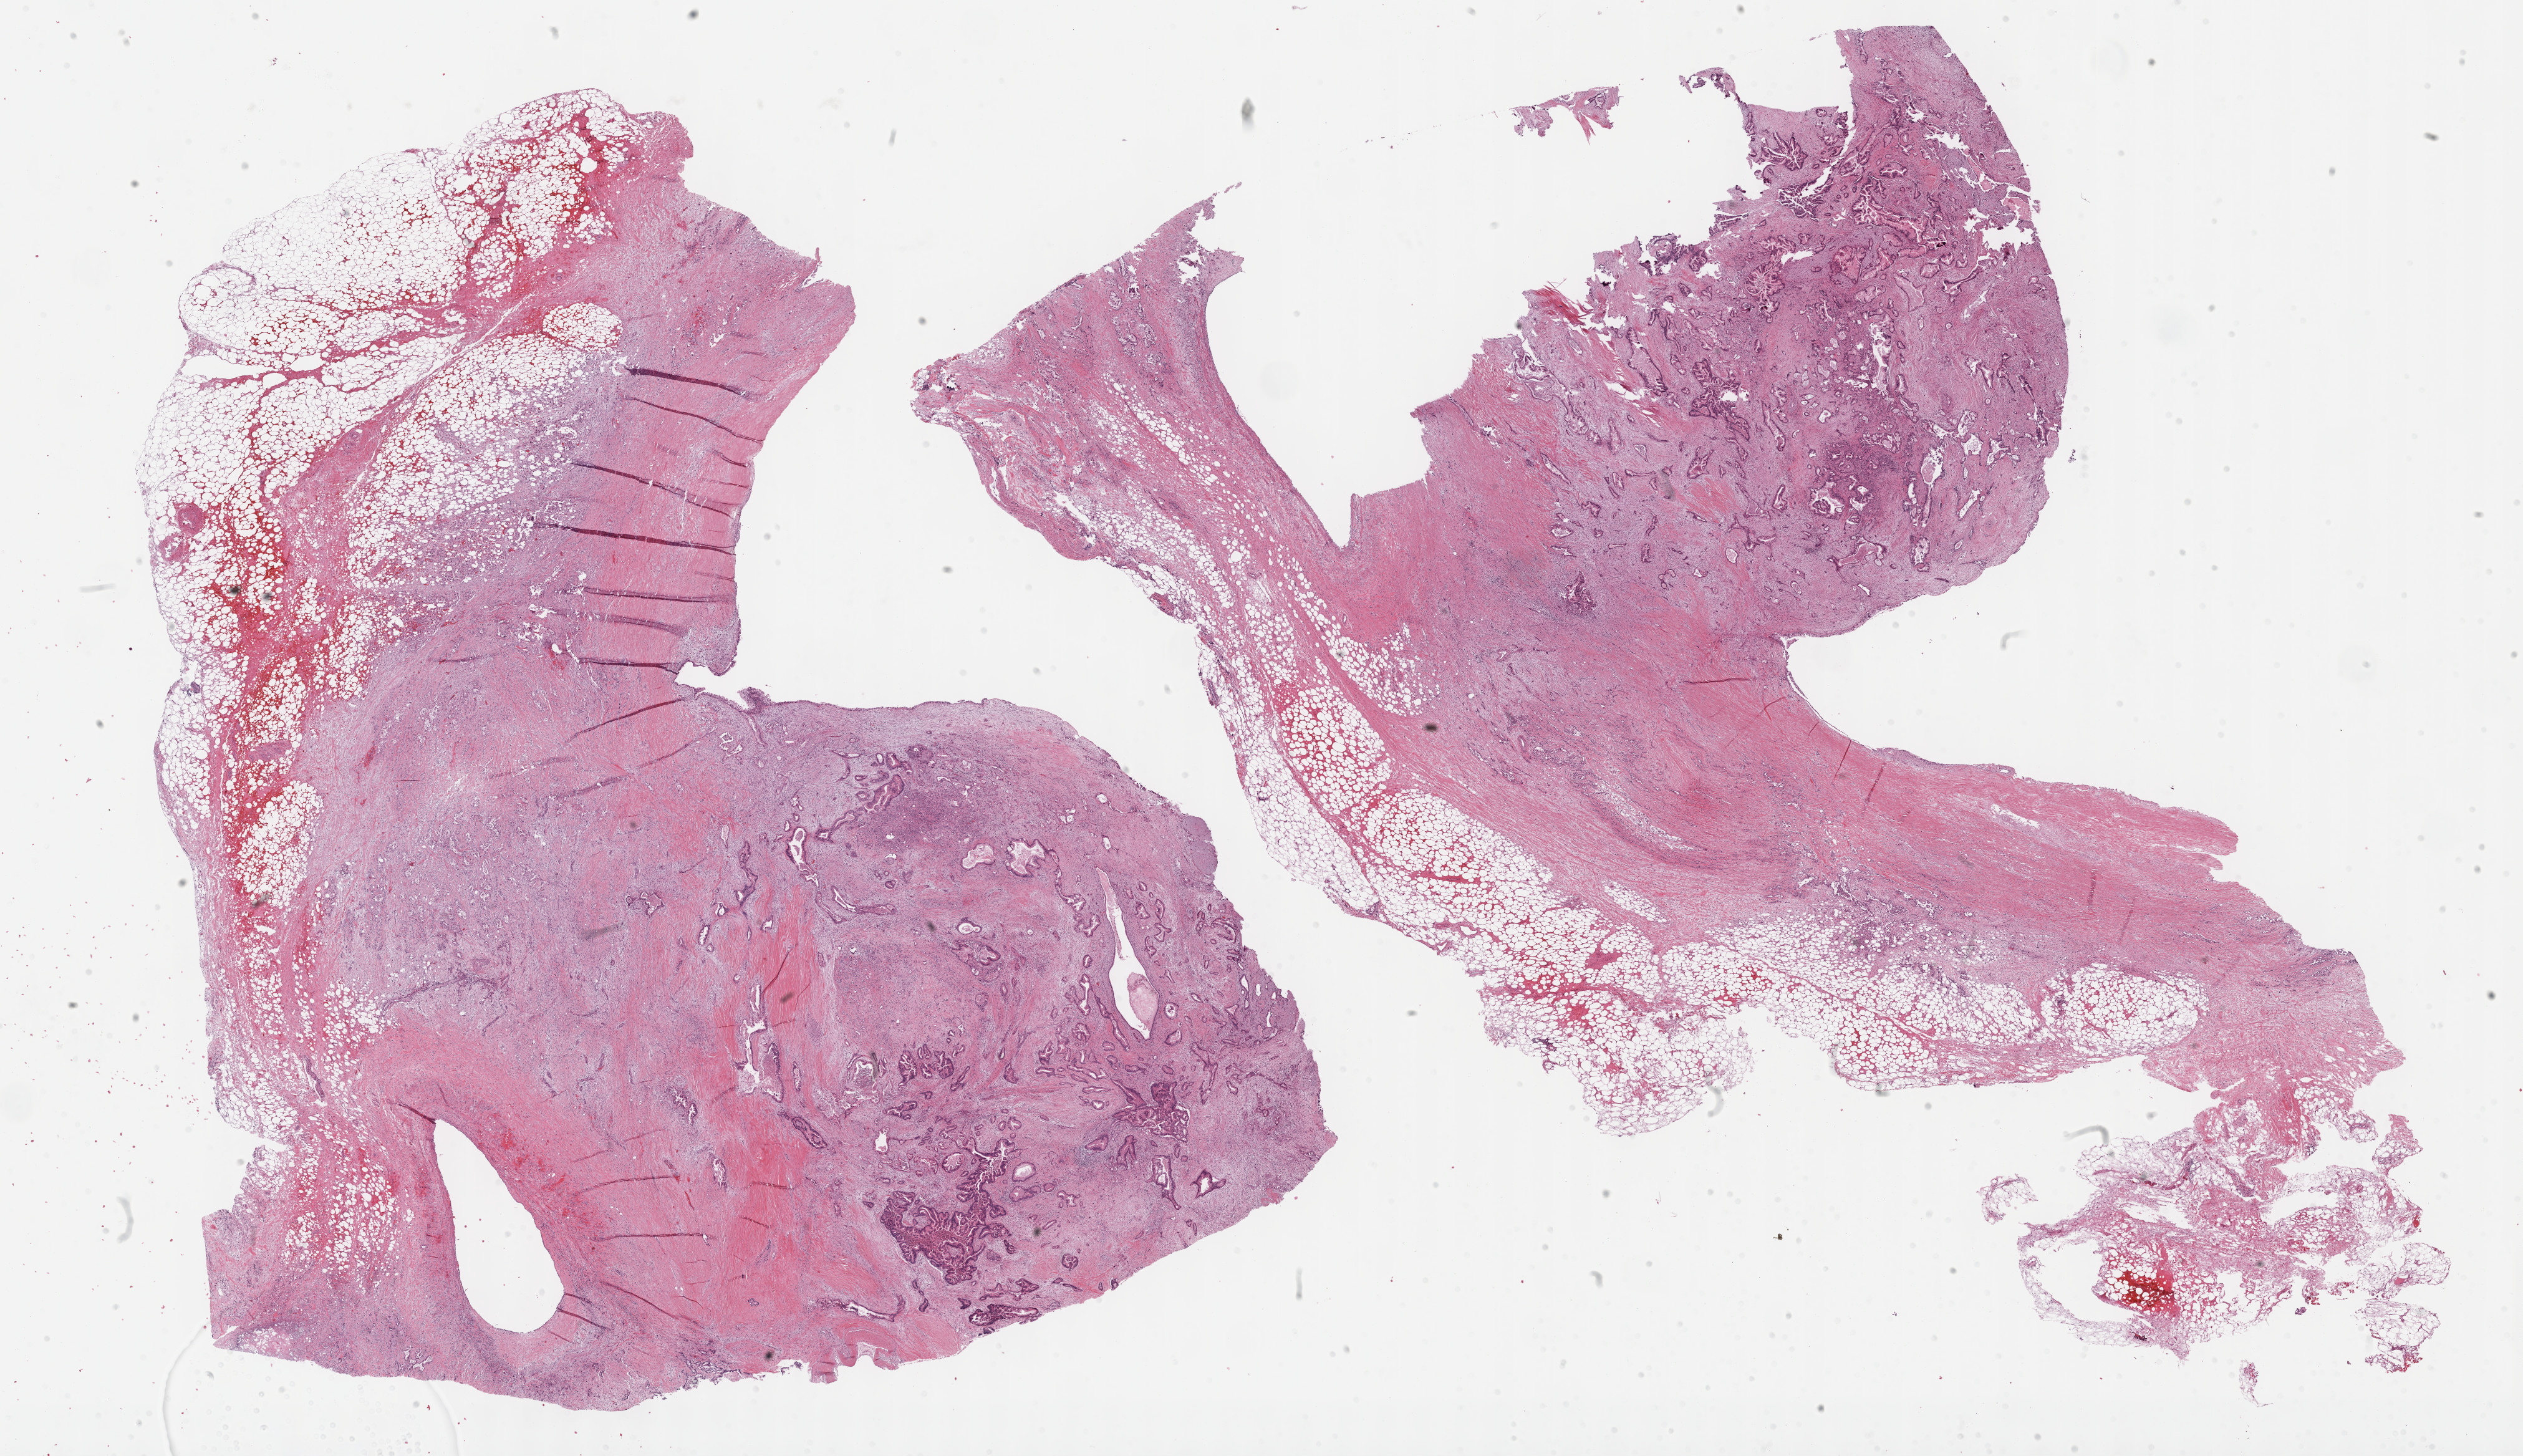
H&E-stained whole-slide image — shown as a low-resolution overview of the whole scanned area (about 32.7 x 18.9 mm), formalin-fixed paraffin-embedded (FFPE) diagnostic section, primary tumour sample from the pancreas. Male, age 75 years at initial diagnosis.
Histologic diagnosis: Infiltrating duct carcinoma, NOS (body of pancreas).